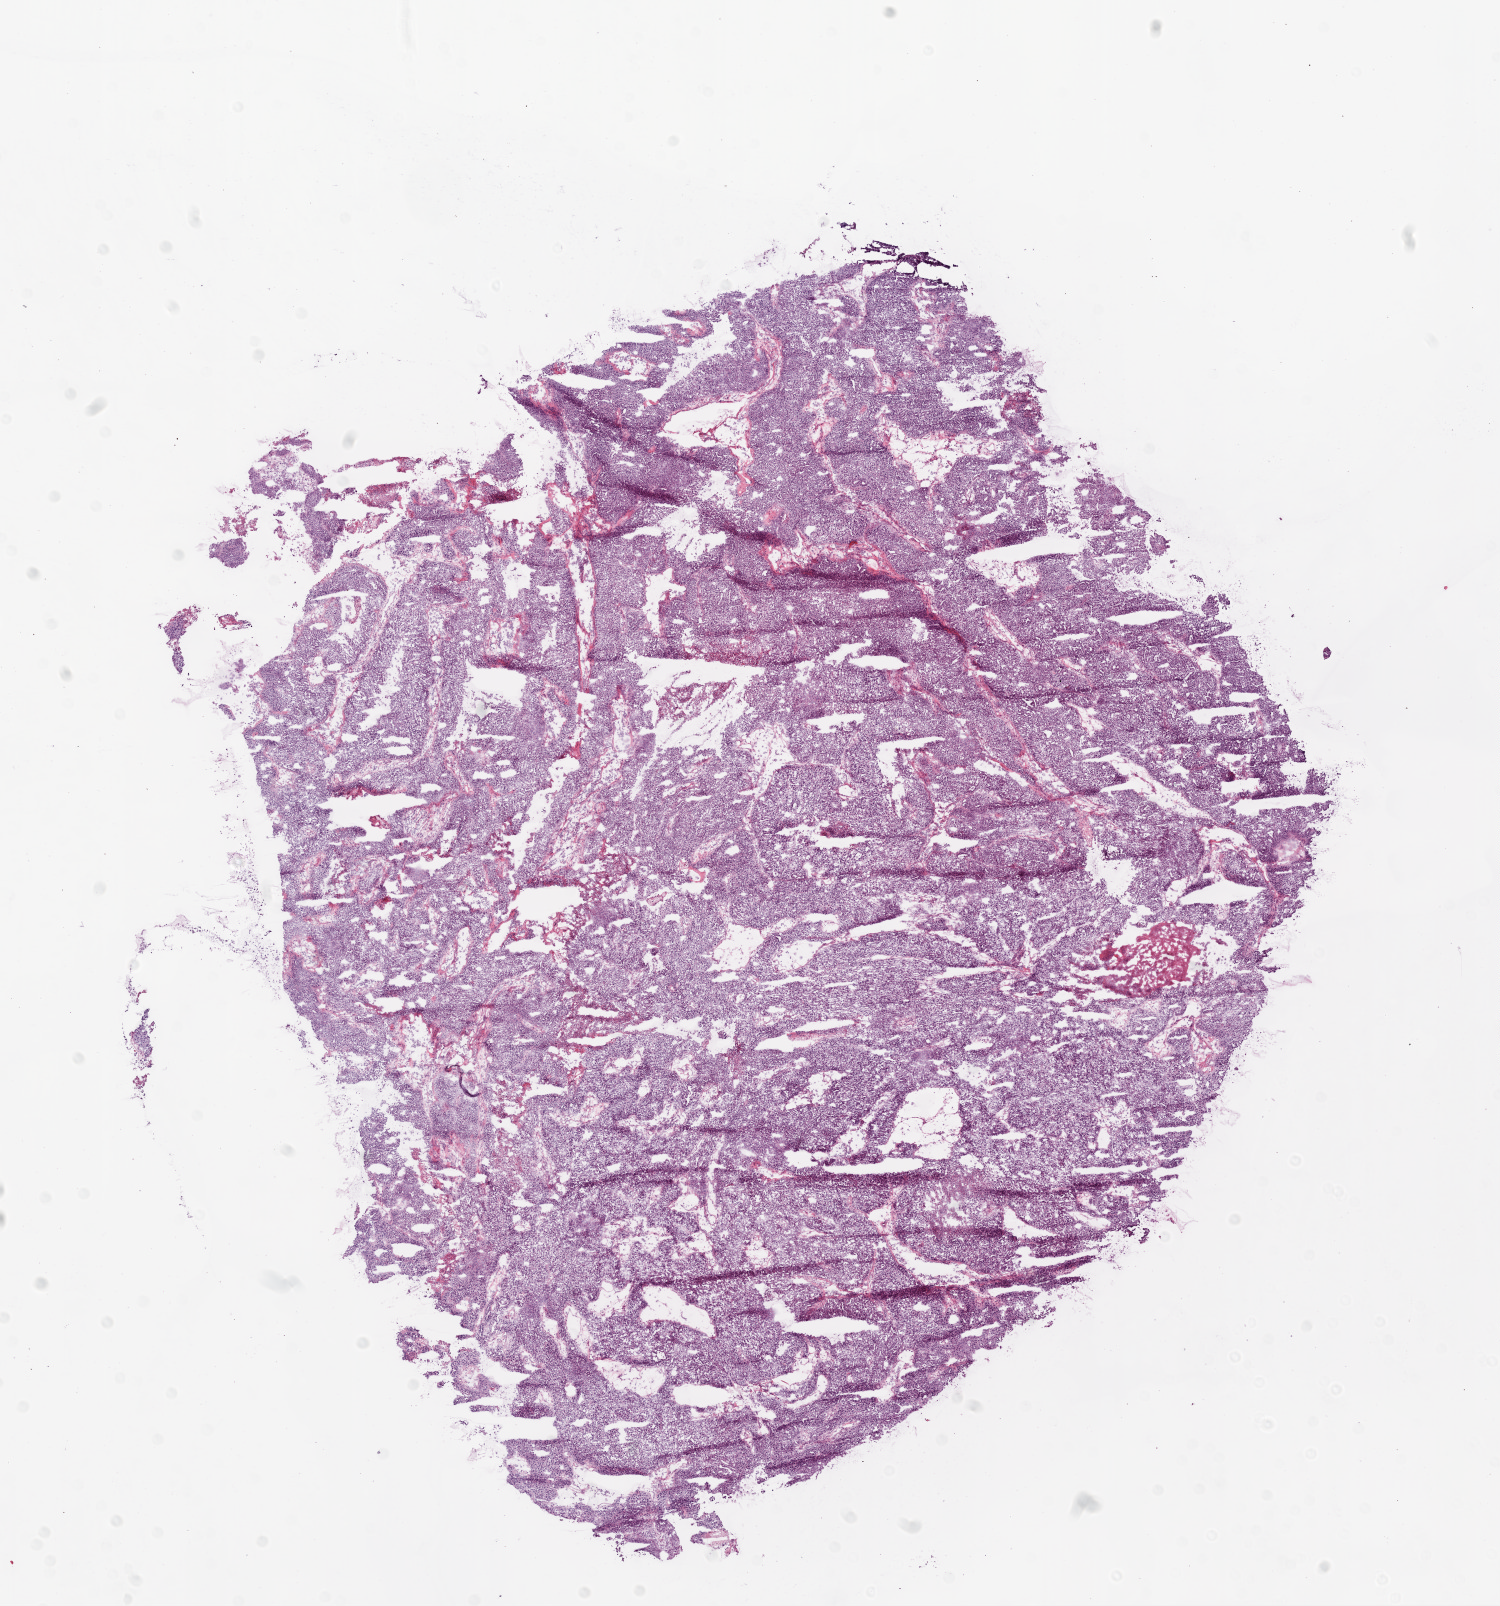
Digitized H&E tissue section (whole slide), shown as a low-resolution overview of the whole scanned area (about 12.0 x 12.9 mm, acquisition: 20x scan), frozen section from the top of the tissue portion, ovary, primary tumour sample. Patient: female, age at initial diagnosis 55 years. Histologic grade: G3 (poorly differentiated). Composition of this section per pathologist review: tumour cells 94%, tumour nuclei 95%, normal cells 0%, stromal cells 5%, necrosis 1%.
Histologic diagnosis: Serous cystadenocarcinoma, NOS. FIGO stage: IB.